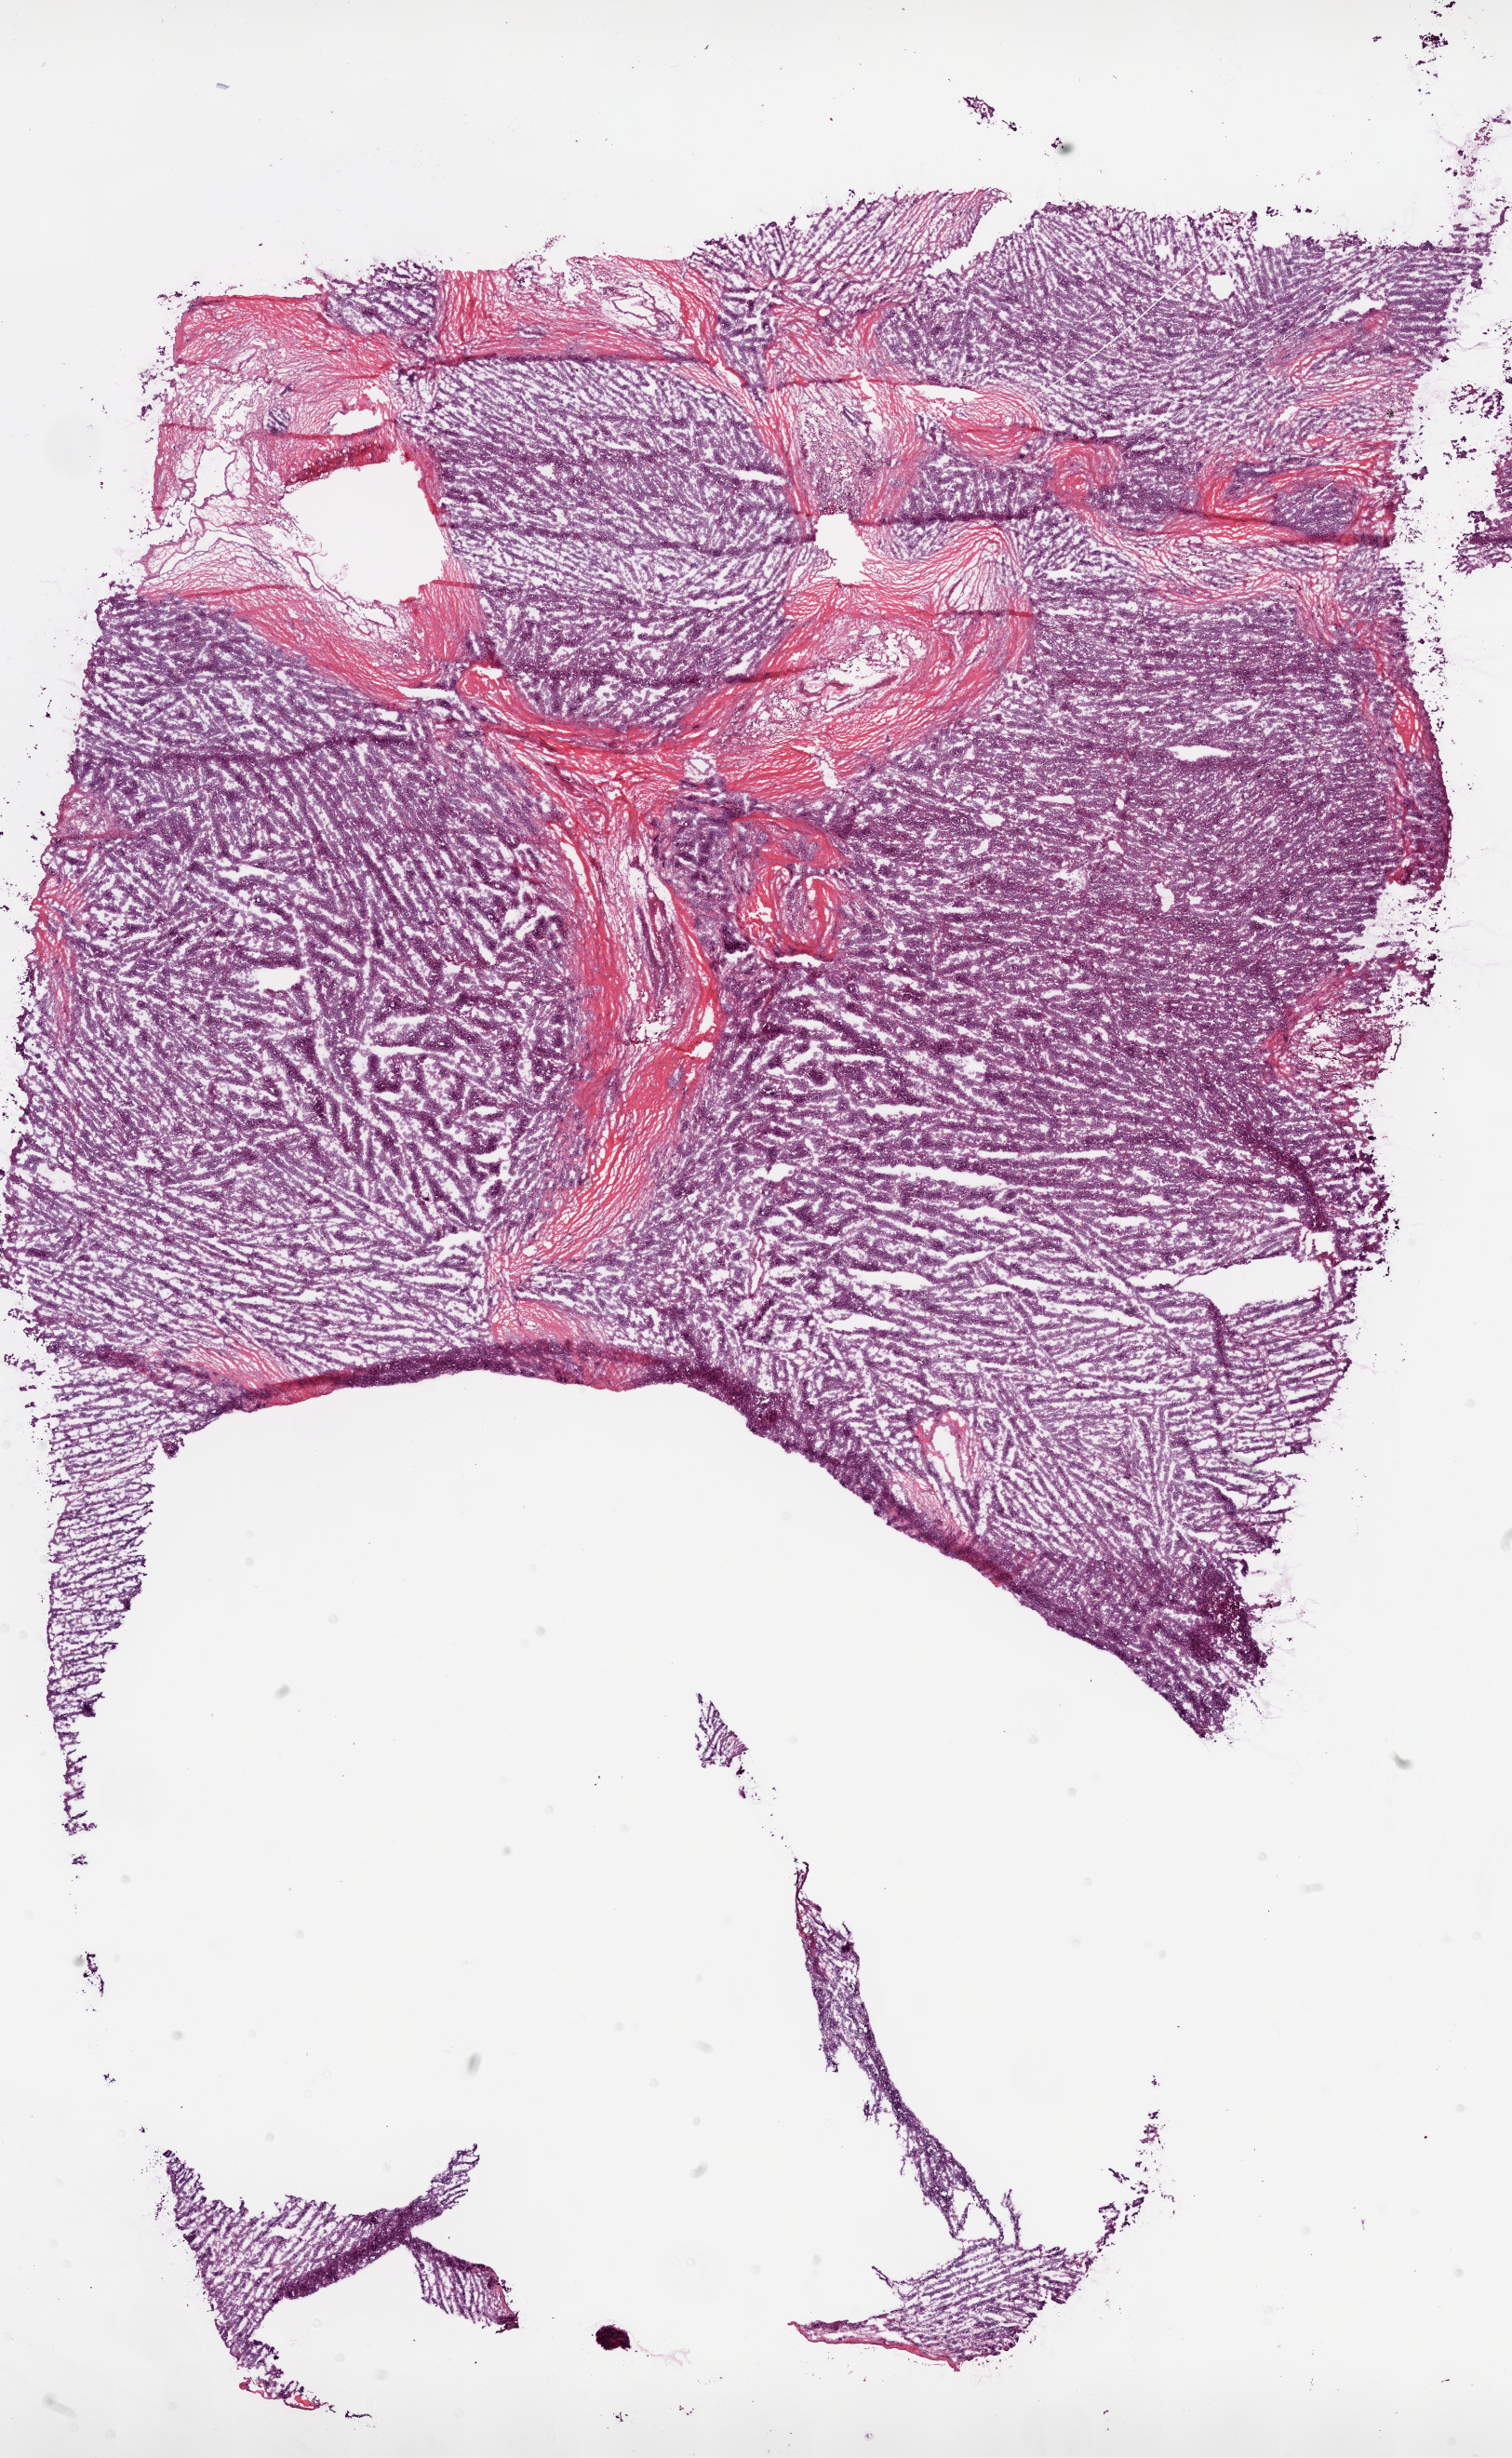
H&E-stained whole-slide image, low-resolution overview of the scanned area, about 13.0 x 21.2 mm (acquisition: 20x scan); frozen section; ovary, primary tumour sample. Female patient; age at initial diagnosis 68 years. Histologic grade: G3 (poorly differentiated). Pathologist review of this section (percent, as recorded): tumour cells 94%, tumour nuclei 95%, normal cells 0%, stromal cells 5%, necrosis 1%.
Histologic diagnosis: Serous cystadenocarcinoma, NOS. Laterality: bilateral. FIGO stage: IIIC.